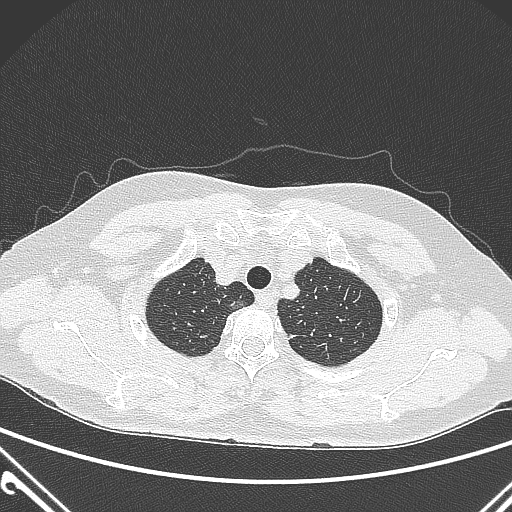
Chest CT, one axial slice; position 247 of 300 along the scan axis; 120 kVp; lung window (W 1500 / L -600 HU); 512 × 512 image matrix, field of view 350 × 350 mm. Patient: female, 54 years. Case-level facts recorded for this patient, not image findings: clinical TNM (as recorded): T1a N0 M0; histopathological grade: G1.
Outlined on this slice (rectangle marked by the reading radiologist):
- lung tumour (recorded histology: adenocarcinoma): bounding box (x1, y1, x2, y2) in pixels: (224, 293, 248, 319)